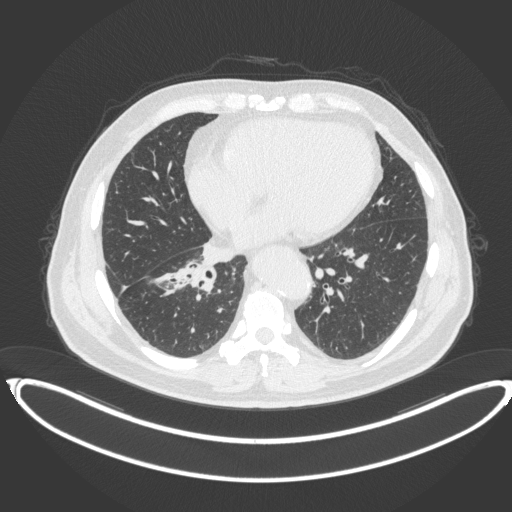
Chest CT, one axial slice. Position 160 of 383 along the scan axis. Reconstruction kernel B31f. Lung window (W 1500 / L -600 HU). 1 mm slice thickness. 512 × 512 image matrix, field of view 448 × 448 mm. Patient: male, 61 years. Case-level facts recorded for this patient, not image findings: clinical TNM (as recorded): T1b N1 M0.
Structures marked on this image (bounding box drawn by a radiologist):
- lung tumour (recorded histology: squamous cell carcinoma): box from (x=174, y=260) to (x=219, y=292) px